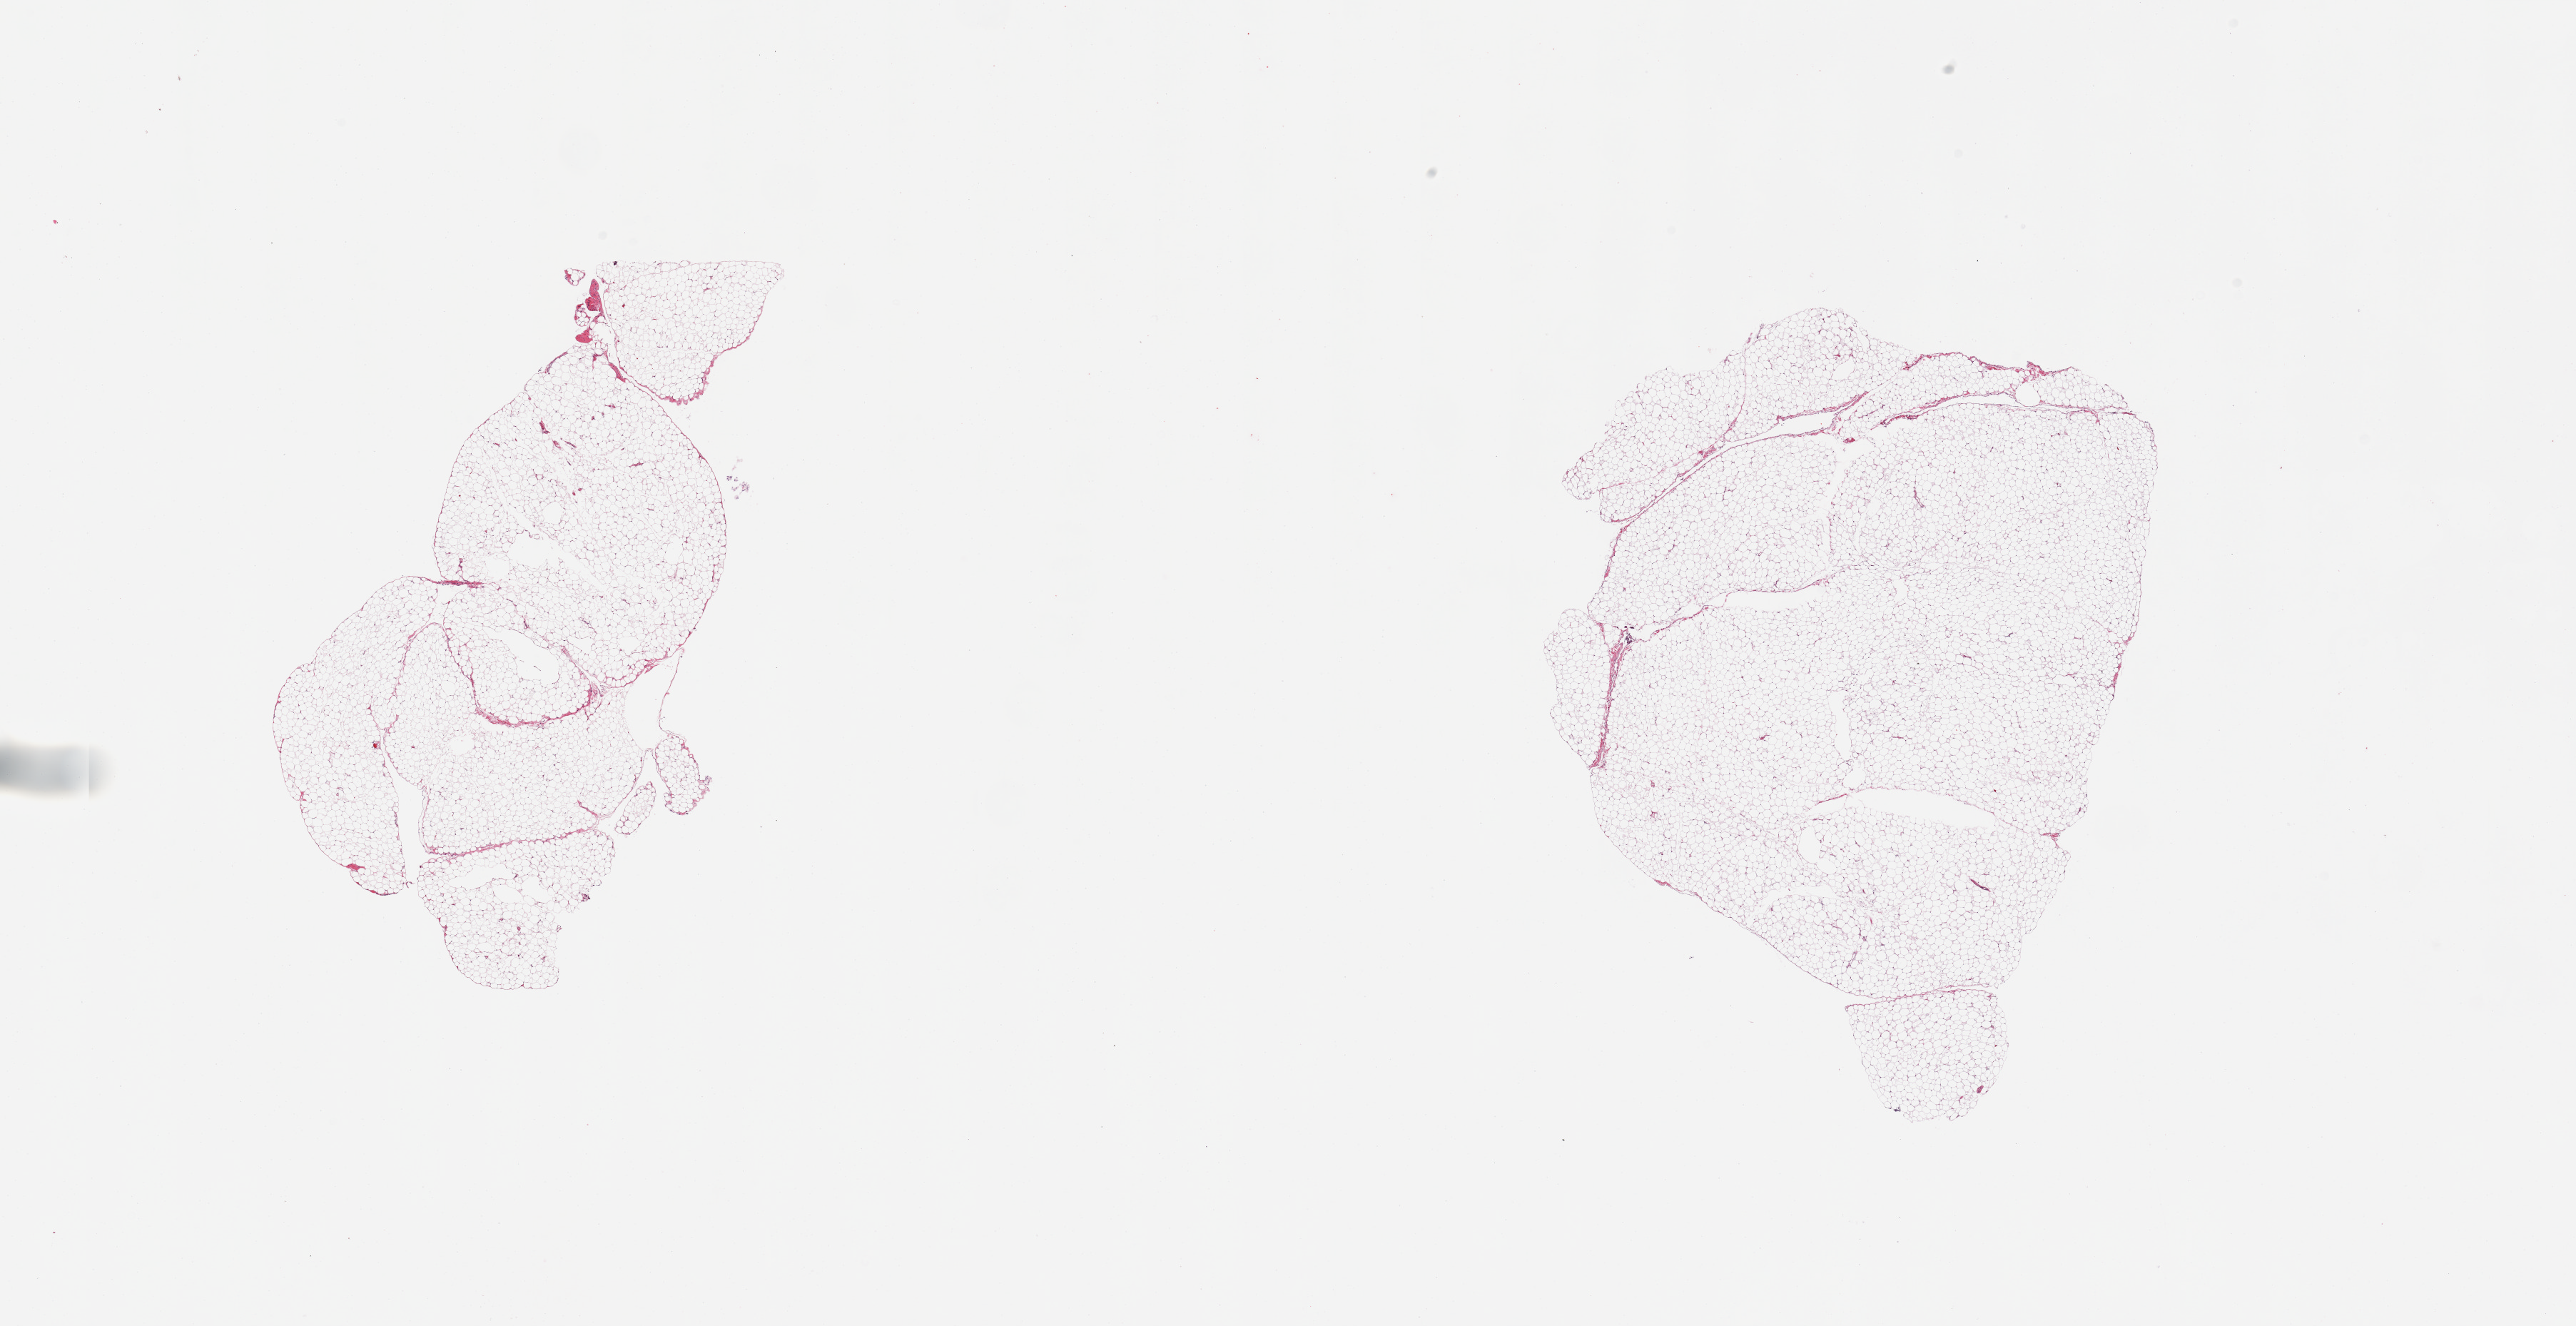
Digitized haematoxylin and eosin-stained section, brightfield, shown as a low-resolution overview of the whole scanned area (about 28.5 x 14.7 mm, from a 20x scan); PAXgene-fixed, paraffin-embedded tissue; target tissue: omentum; tissue donor sample. Donor: male.
Review note (as recorded): 2 pieces; mature adipose tissue.